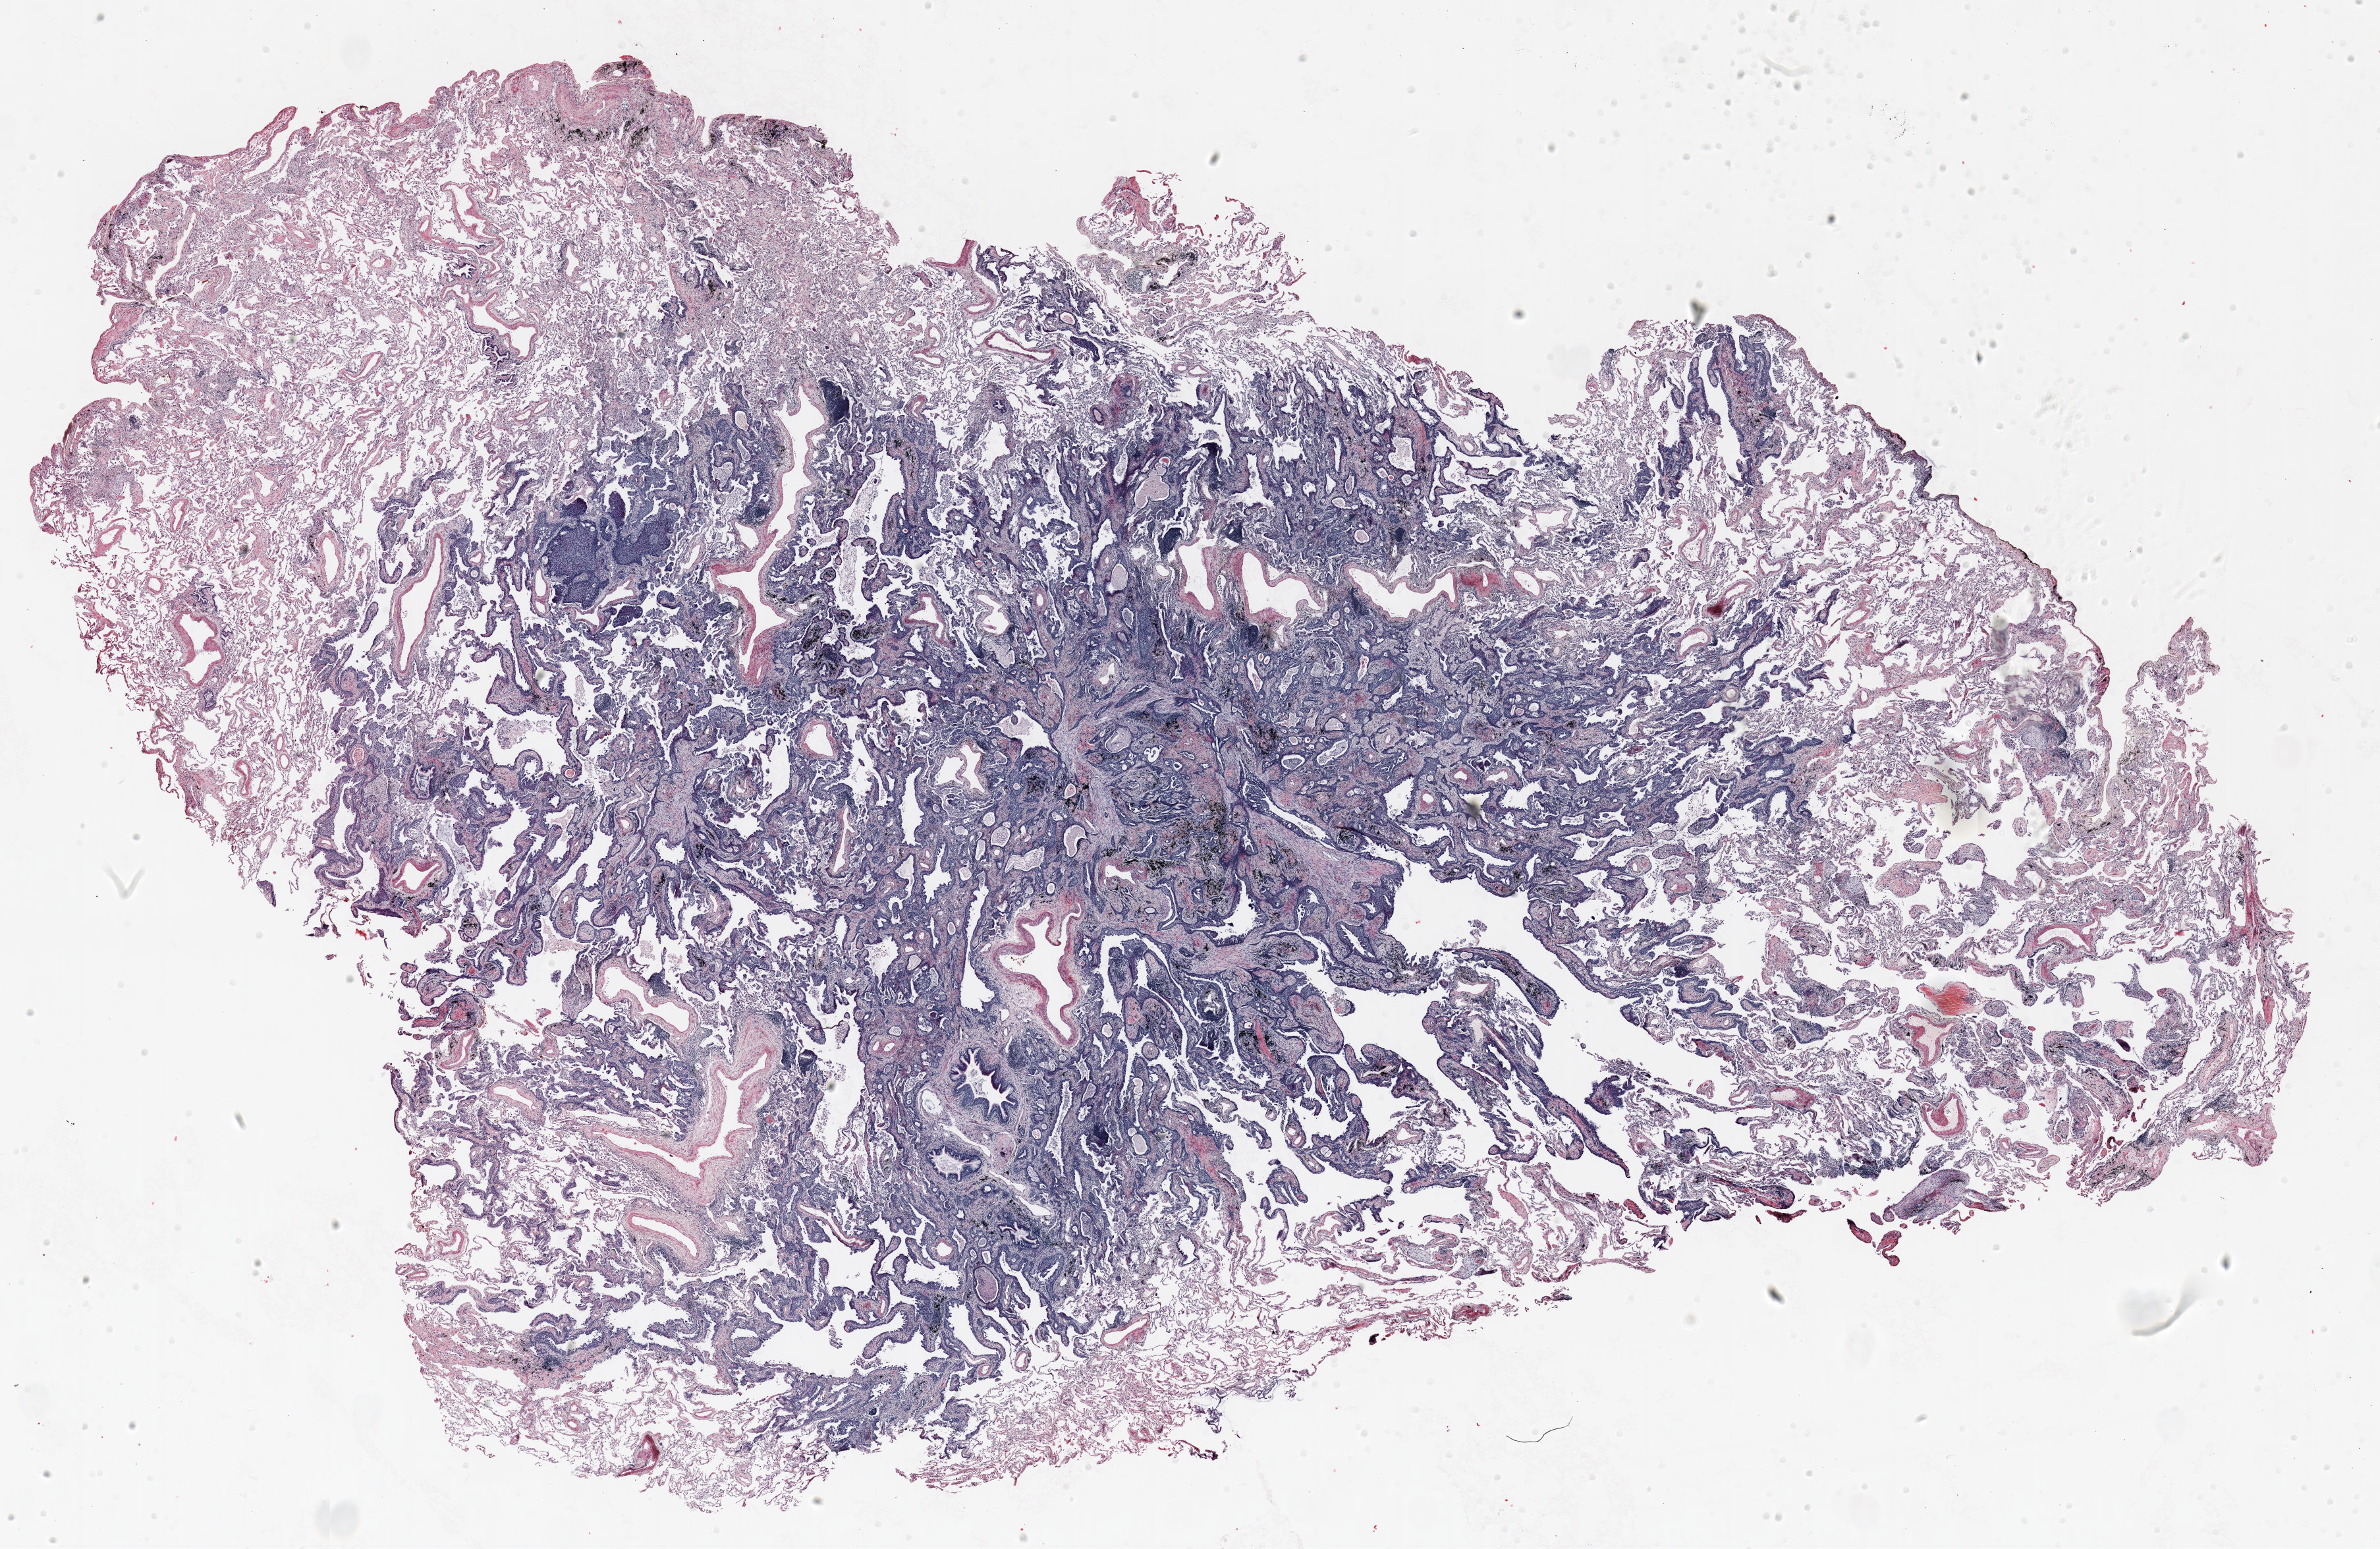
Hematoxylin and eosin (H&E) stained whole-slide image, a low-resolution overview of the entire scanned area, about 29.0 x 18.9 mm (acquisition: 20x scan), FFPE section, lung tissue. Male patient, aged 67 at enrolment. Grade: moderately differentiated (G2).
* participant's lung-cancer diagnosis: Squamous cell carcinoma, NOS
* primary tumour location (clinical record): right lower lobe
* ICD-O-3 topography: lower lobe of lung (C34.3)
* stage (AJCC 6th edition): IA
* tumour size (pathology): 23 mm